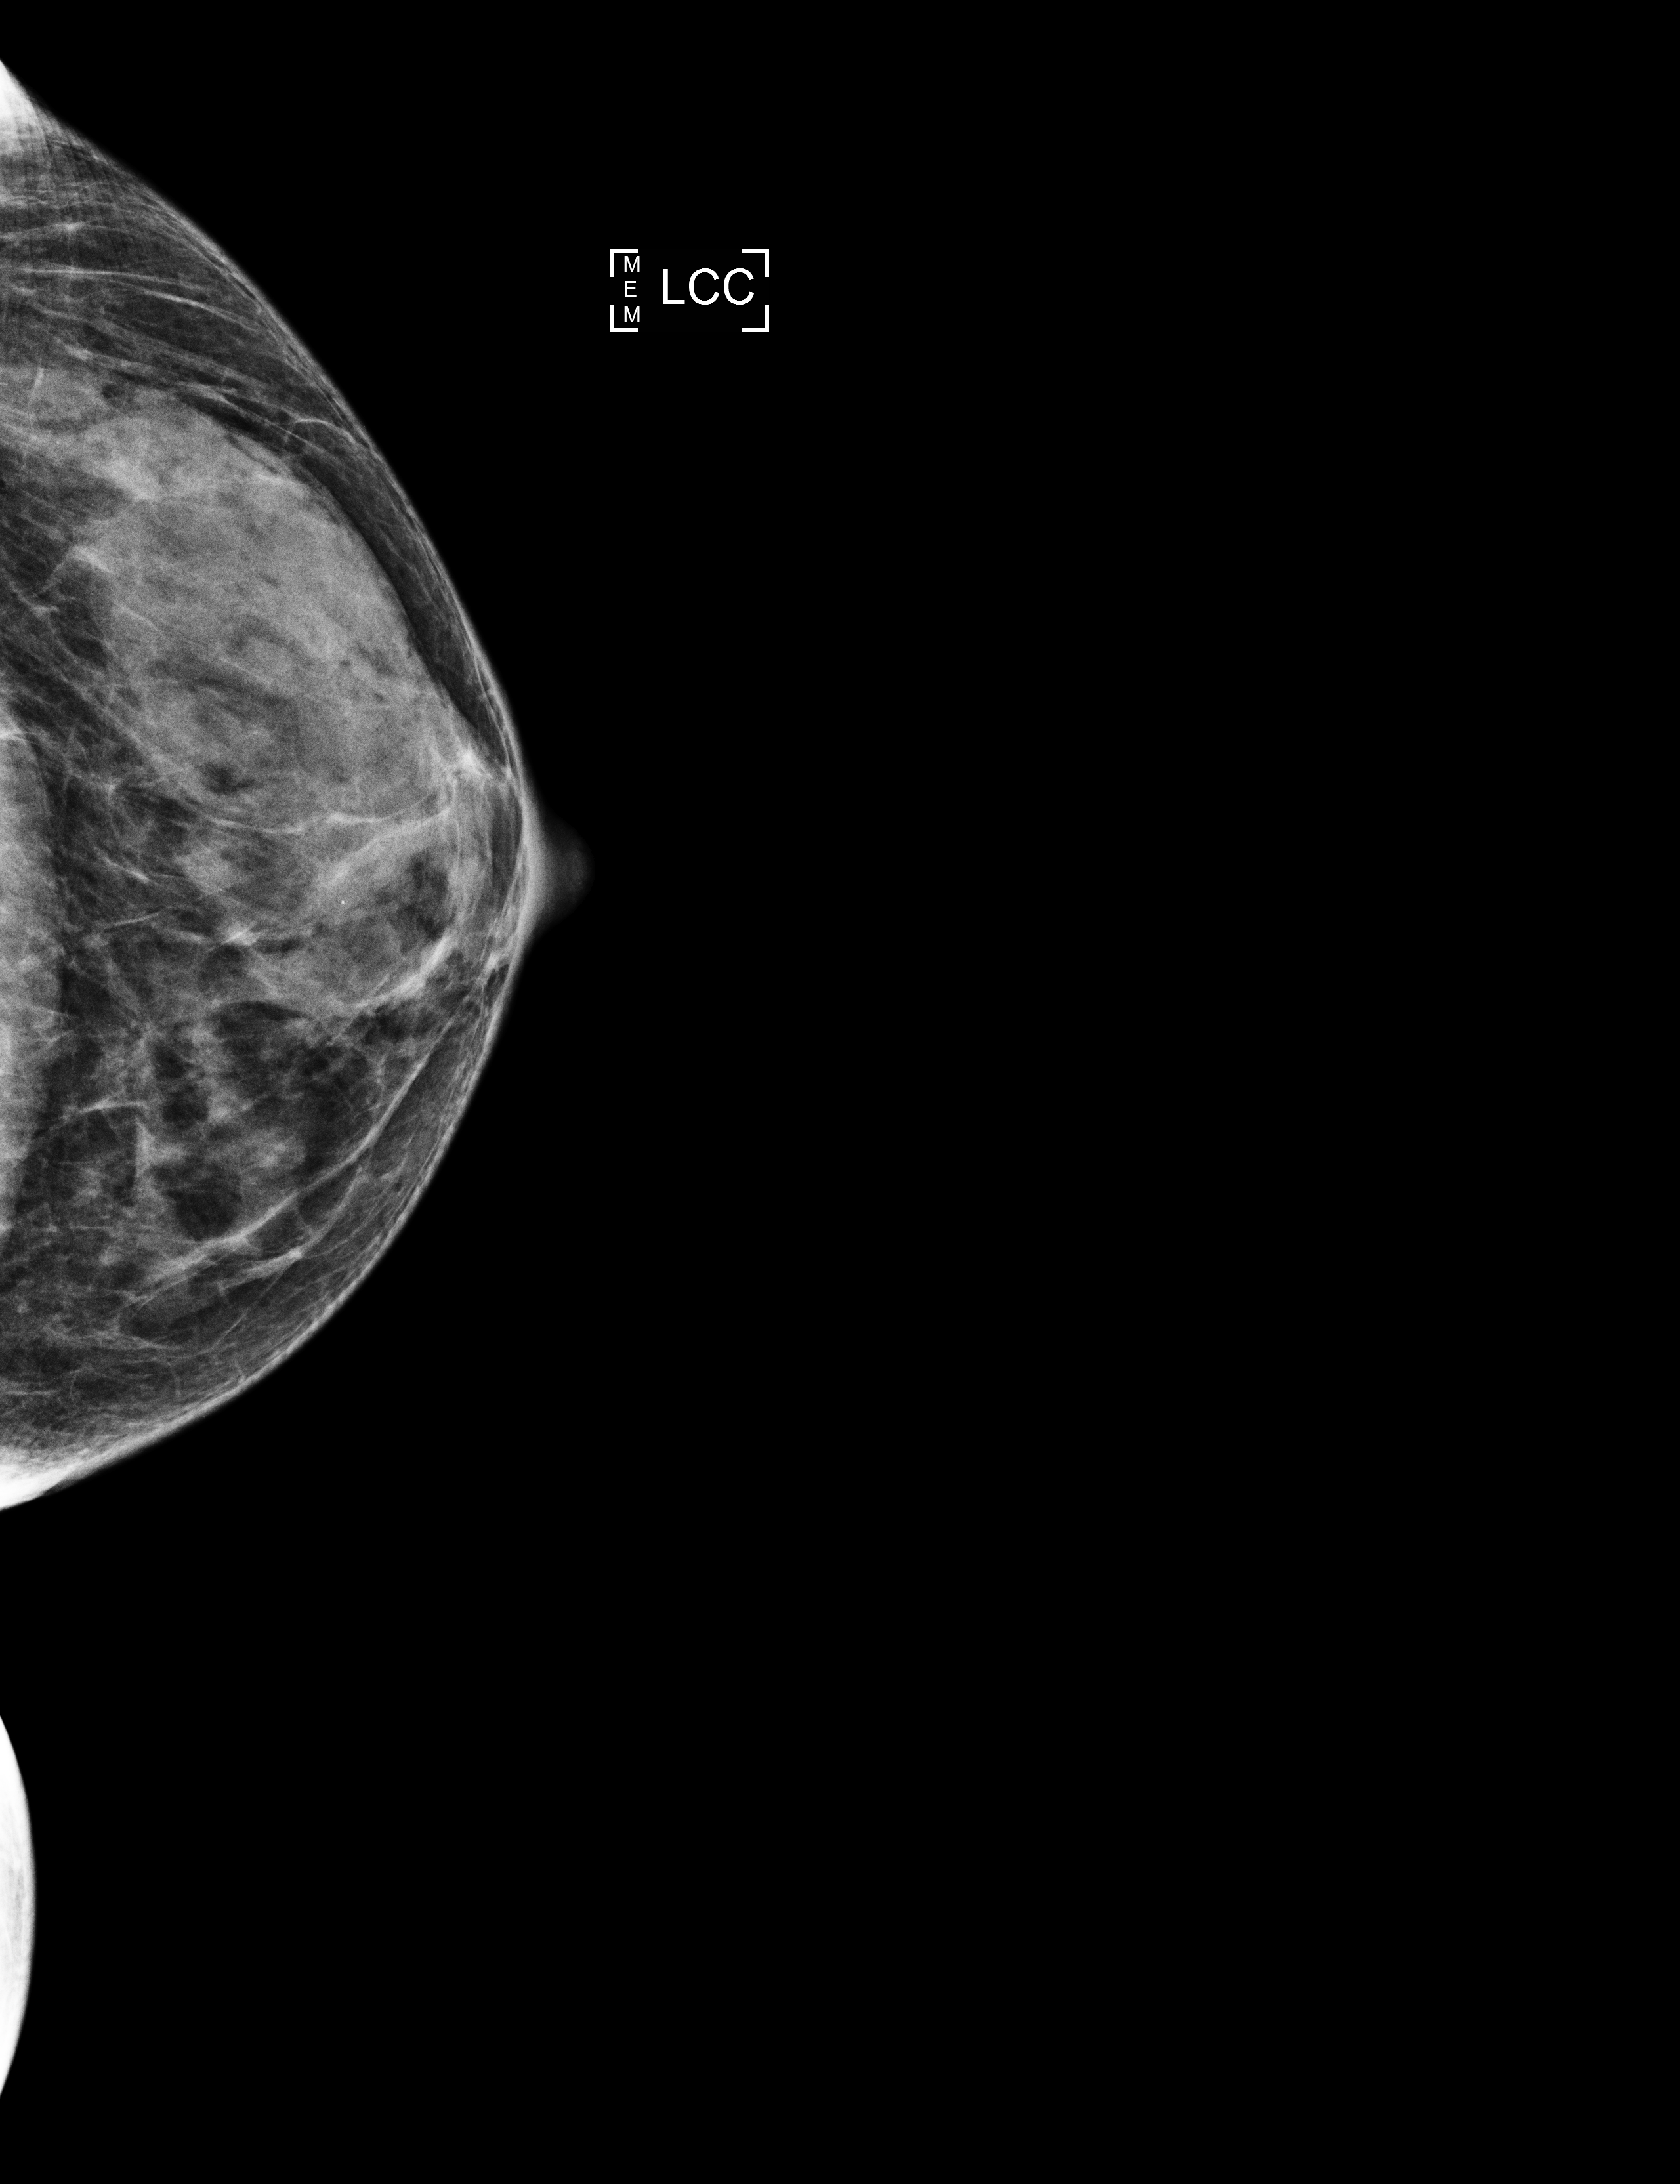
Screening examination, system: Selenia Dimensions. Patient: female, 60 years.
Image type: full-field digital mammogram. Breast: left. Projection: CC view. BI-RADS breast density category at the screening exam (both breasts, scale 1–4): 3. Final BI-RADS assessment for this screening round (tomosynthesis exam, both breasts): category 1. Recall: no recall after this screen.